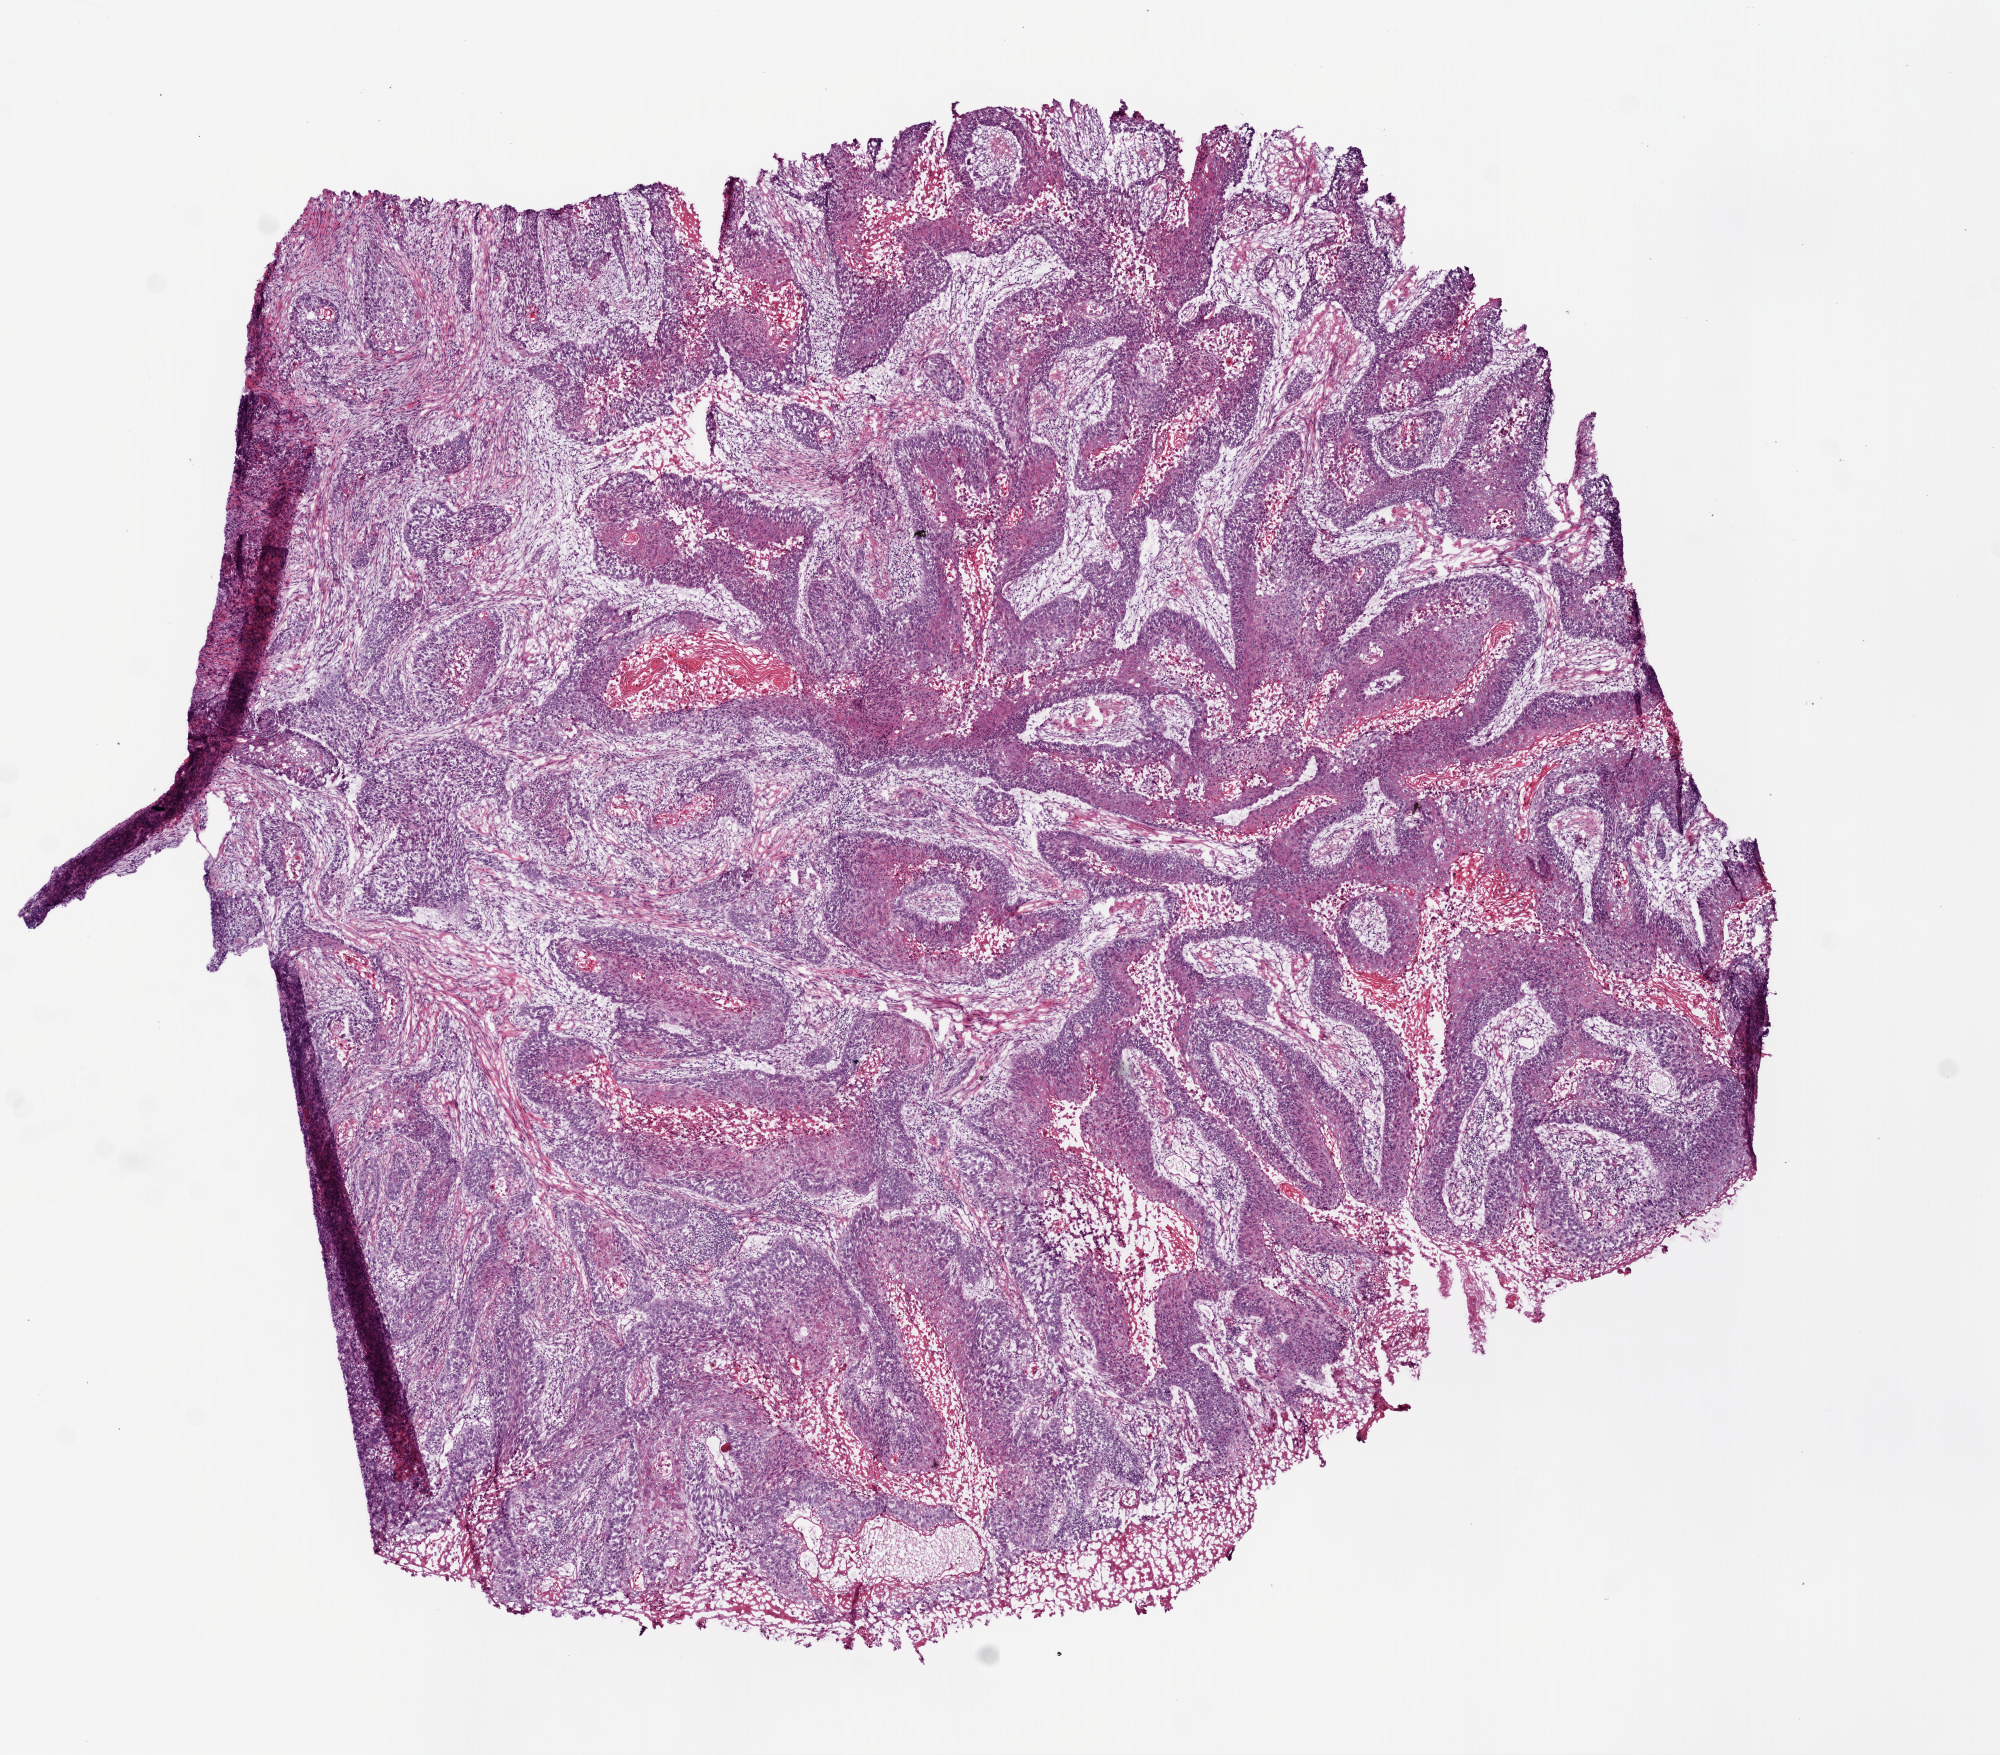
Digitized H&E tissue section (whole slide), shown as a low-resolution overview of the whole scanned area (about 8.0 x 7.0 mm, from a 20x scan). Frozen section from the bottom of the tissue portion. Sample: primary tumour, head and neck. Male patient; age at initial diagnosis 87 years. Histologic grade: G2 (moderately differentiated). Pathologist review of this section (percent, as recorded): tumour cells 93%, tumour nuclei 70%, normal cells 0%, stromal cells 0%, necrosis 7%. Inflammatory infiltration, as recorded: lymphocyte infiltration 15%, monocyte infiltration 1%, neutrophil infiltration 1%.
TNM: T3 N0. Pathologic diagnosis: Squamous cell carcinoma, NOS (overlapping lesion of lip, oral cavity and pharynx). Lymph nodes positive (case pathology): 0 of 31 examined. AJCC pathologic stage: III.